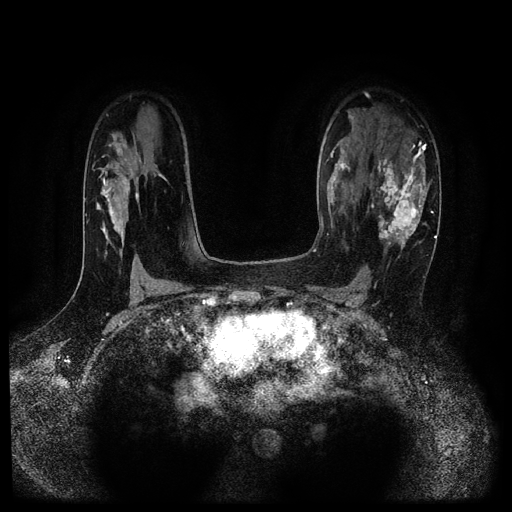
Breast MRI (dynamic contrast-enhanced, multi-phase), one axial slice; slice 70 of 116 in the series (ordered by position); dynamic contrast-enhanced series, time point 2 of 5 at this slice position (early post-contrast); 1.5 T; TE 2.7 ms, TR 5.4 ms; 2.2 mm slice thickness; 512 × 512 image matrix. Female patient, age 43 years.
Outlined on this slice (semi-automatic segmentation, software-assisted and operator-edited):
- breast lesion (labelled 'tumour' in the annotation; benign lesions carry a separate 'benign' label): bounding box <373,158,425,258> (left, top, right, bottom; pixels)